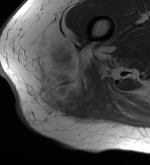
MRI of an extremity soft-tissue mass, one axial slice; position 13 of 56 along the scan axis; MR volume resampled by the dataset authors to the PET/CT grid (not the native acquisition matrix); 3.27 mm slice thickness; 150 × 165 image matrix, field of view 146 × 161 mm. Female patient. Case-level facts recorded for this patient, not image findings: histological type: epithelioid sarcoma with vascular differentiation; site of the primary tumour: right buttock.
Annotated regions visible in this slice (expert contour drawn on MRI and transferred to this co-registered scan by the dataset authors):
- gross tumour volume (mass): bounding box <39,44,85,112> (left, top, right, bottom; pixels)